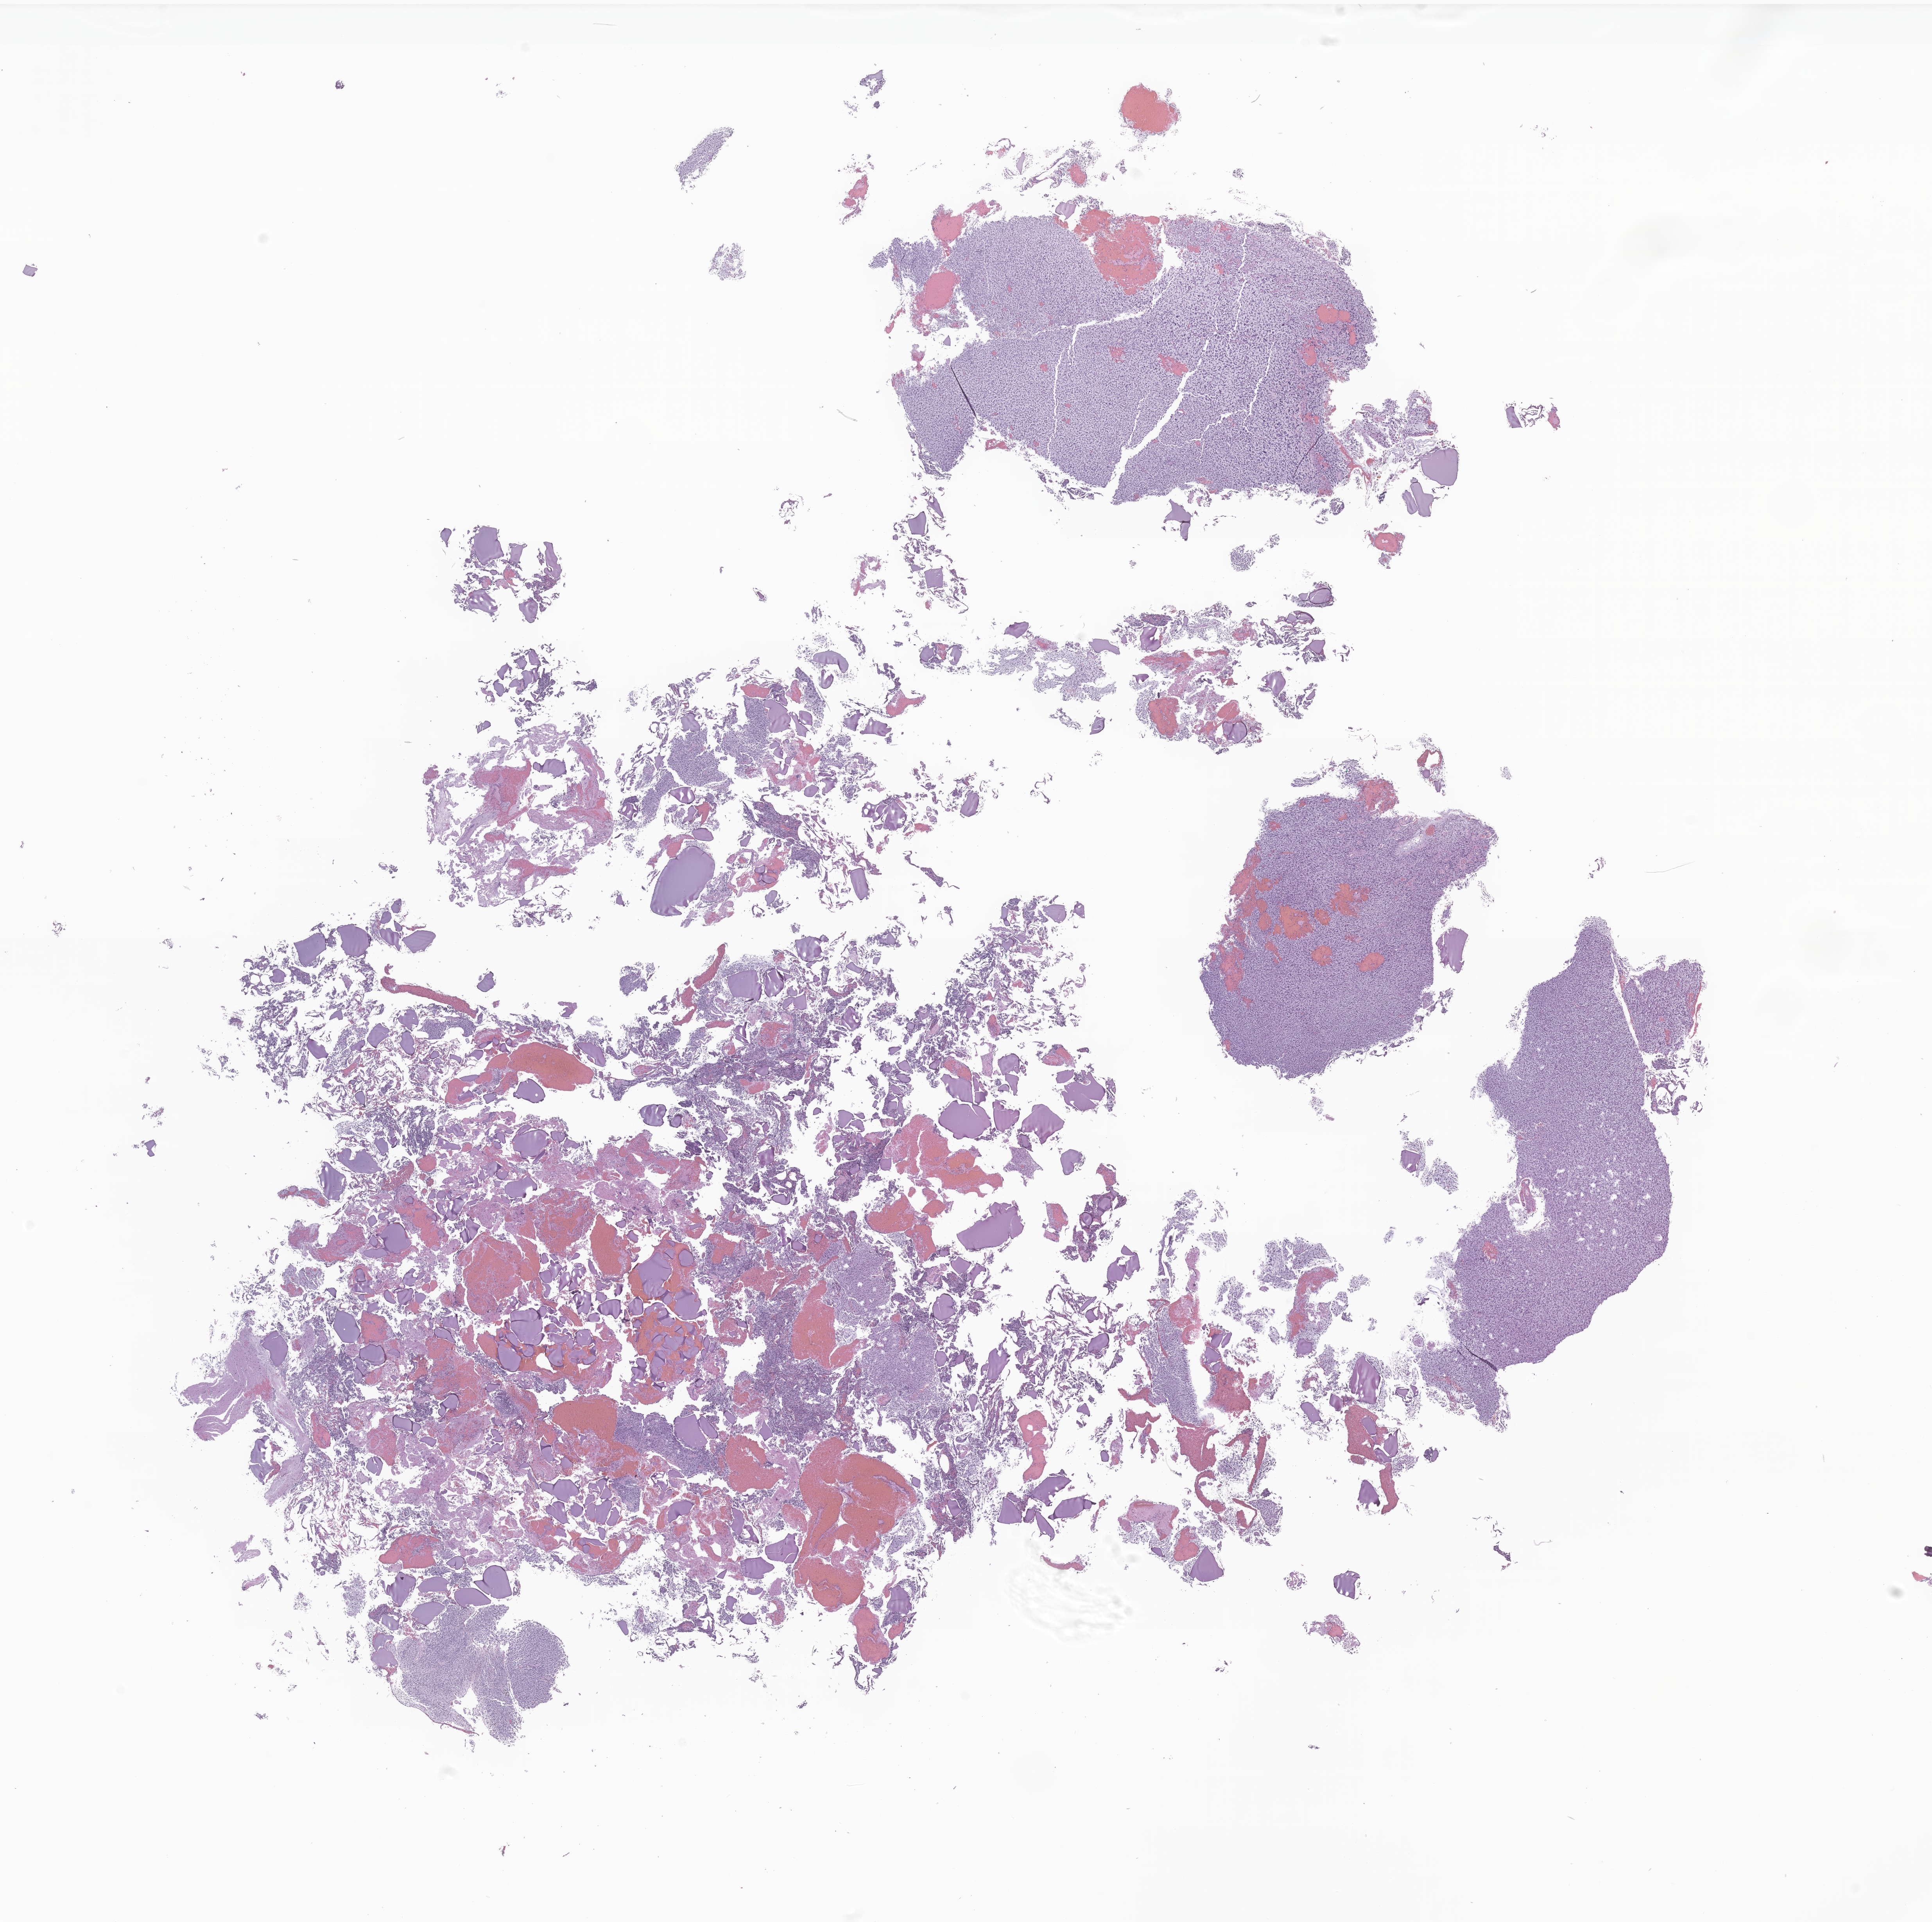
H&E whole-slide image of tumor tissue from the brain — shown as a low-resolution overview of the whole scanned area (about 20.8 x 20.7 mm); formalin-fixed paraffin-embedded section. Female patient, age 118 months.
Diagnosis: Neoplasm, uncertain whether benign or malignant.